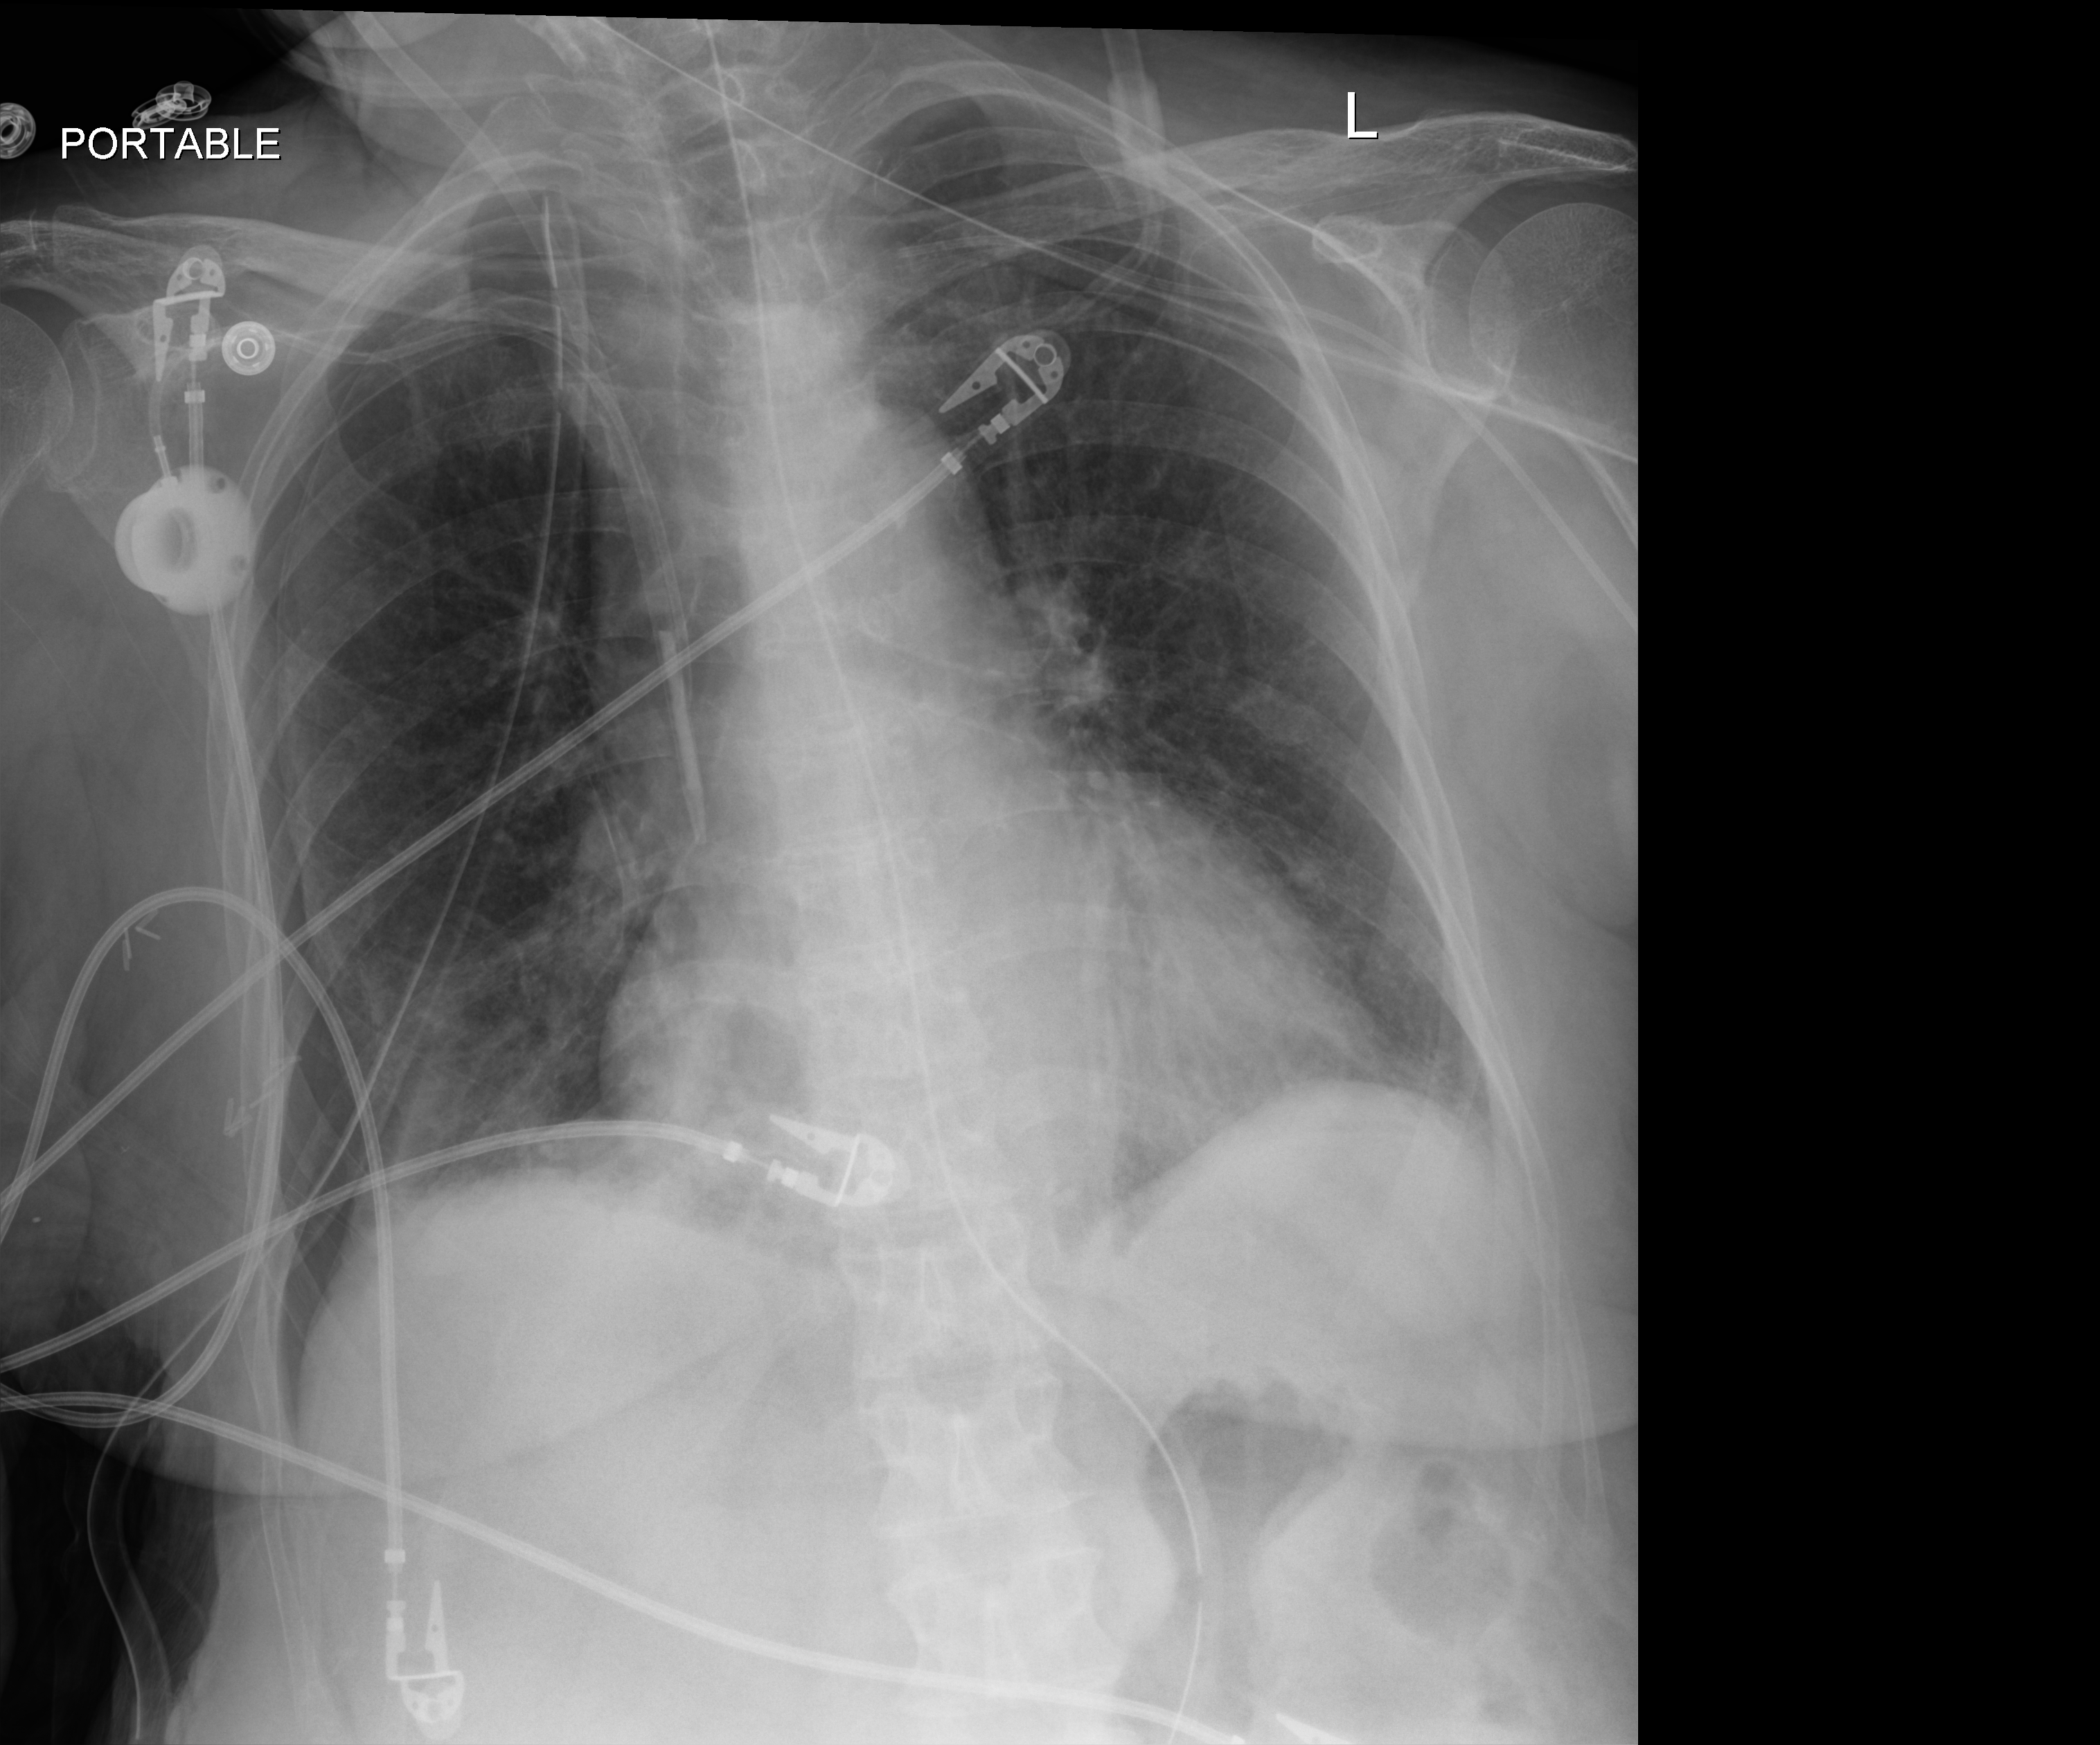
Chest radiograph (digital radiography), anteroposterior (AP) projection. Patient hospitalised with COVID-19; female, aged 60–74 years.
Hospital-stay facts (about this admission, not read from this image; timing relative to this image not recorded): admitted to intensive care during this hospital stay: yes; mechanically ventilated during this hospital stay: yes; hypertension (admission record): yes.